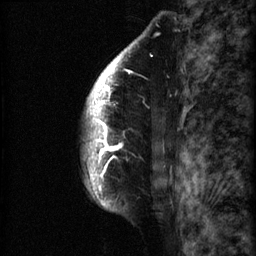
Breast MRI (dynamic contrast-enhanced), one sagittal slice. Position 53 of 60 along the scan axis. 3 images stored at this slice position (order not interpretable as contrast timing). 1.5 T. TE 4.2 ms, TR 22.7 ms. 256 × 256 image matrix, field of view 180 × 180 mm. Female patient, age 48 years. From the clinical record (not read from this slice): setting: breast cancer imaged before/during neoadjuvant chemotherapy; receptor status: triple-negative.
Structures marked on this image (semi-automatic segmentation, software-assisted and operator-edited):
- analysis volume of interest (the breast-tissue region the enhancement analysis was run in; not a lesion): bounding box <82,30,173,207> (left, top, right, bottom; pixels)
- tumour enhancement mask (voxels above the 90 % enhancement threshold inside the analysis volume of interest): <84,43,139,206>